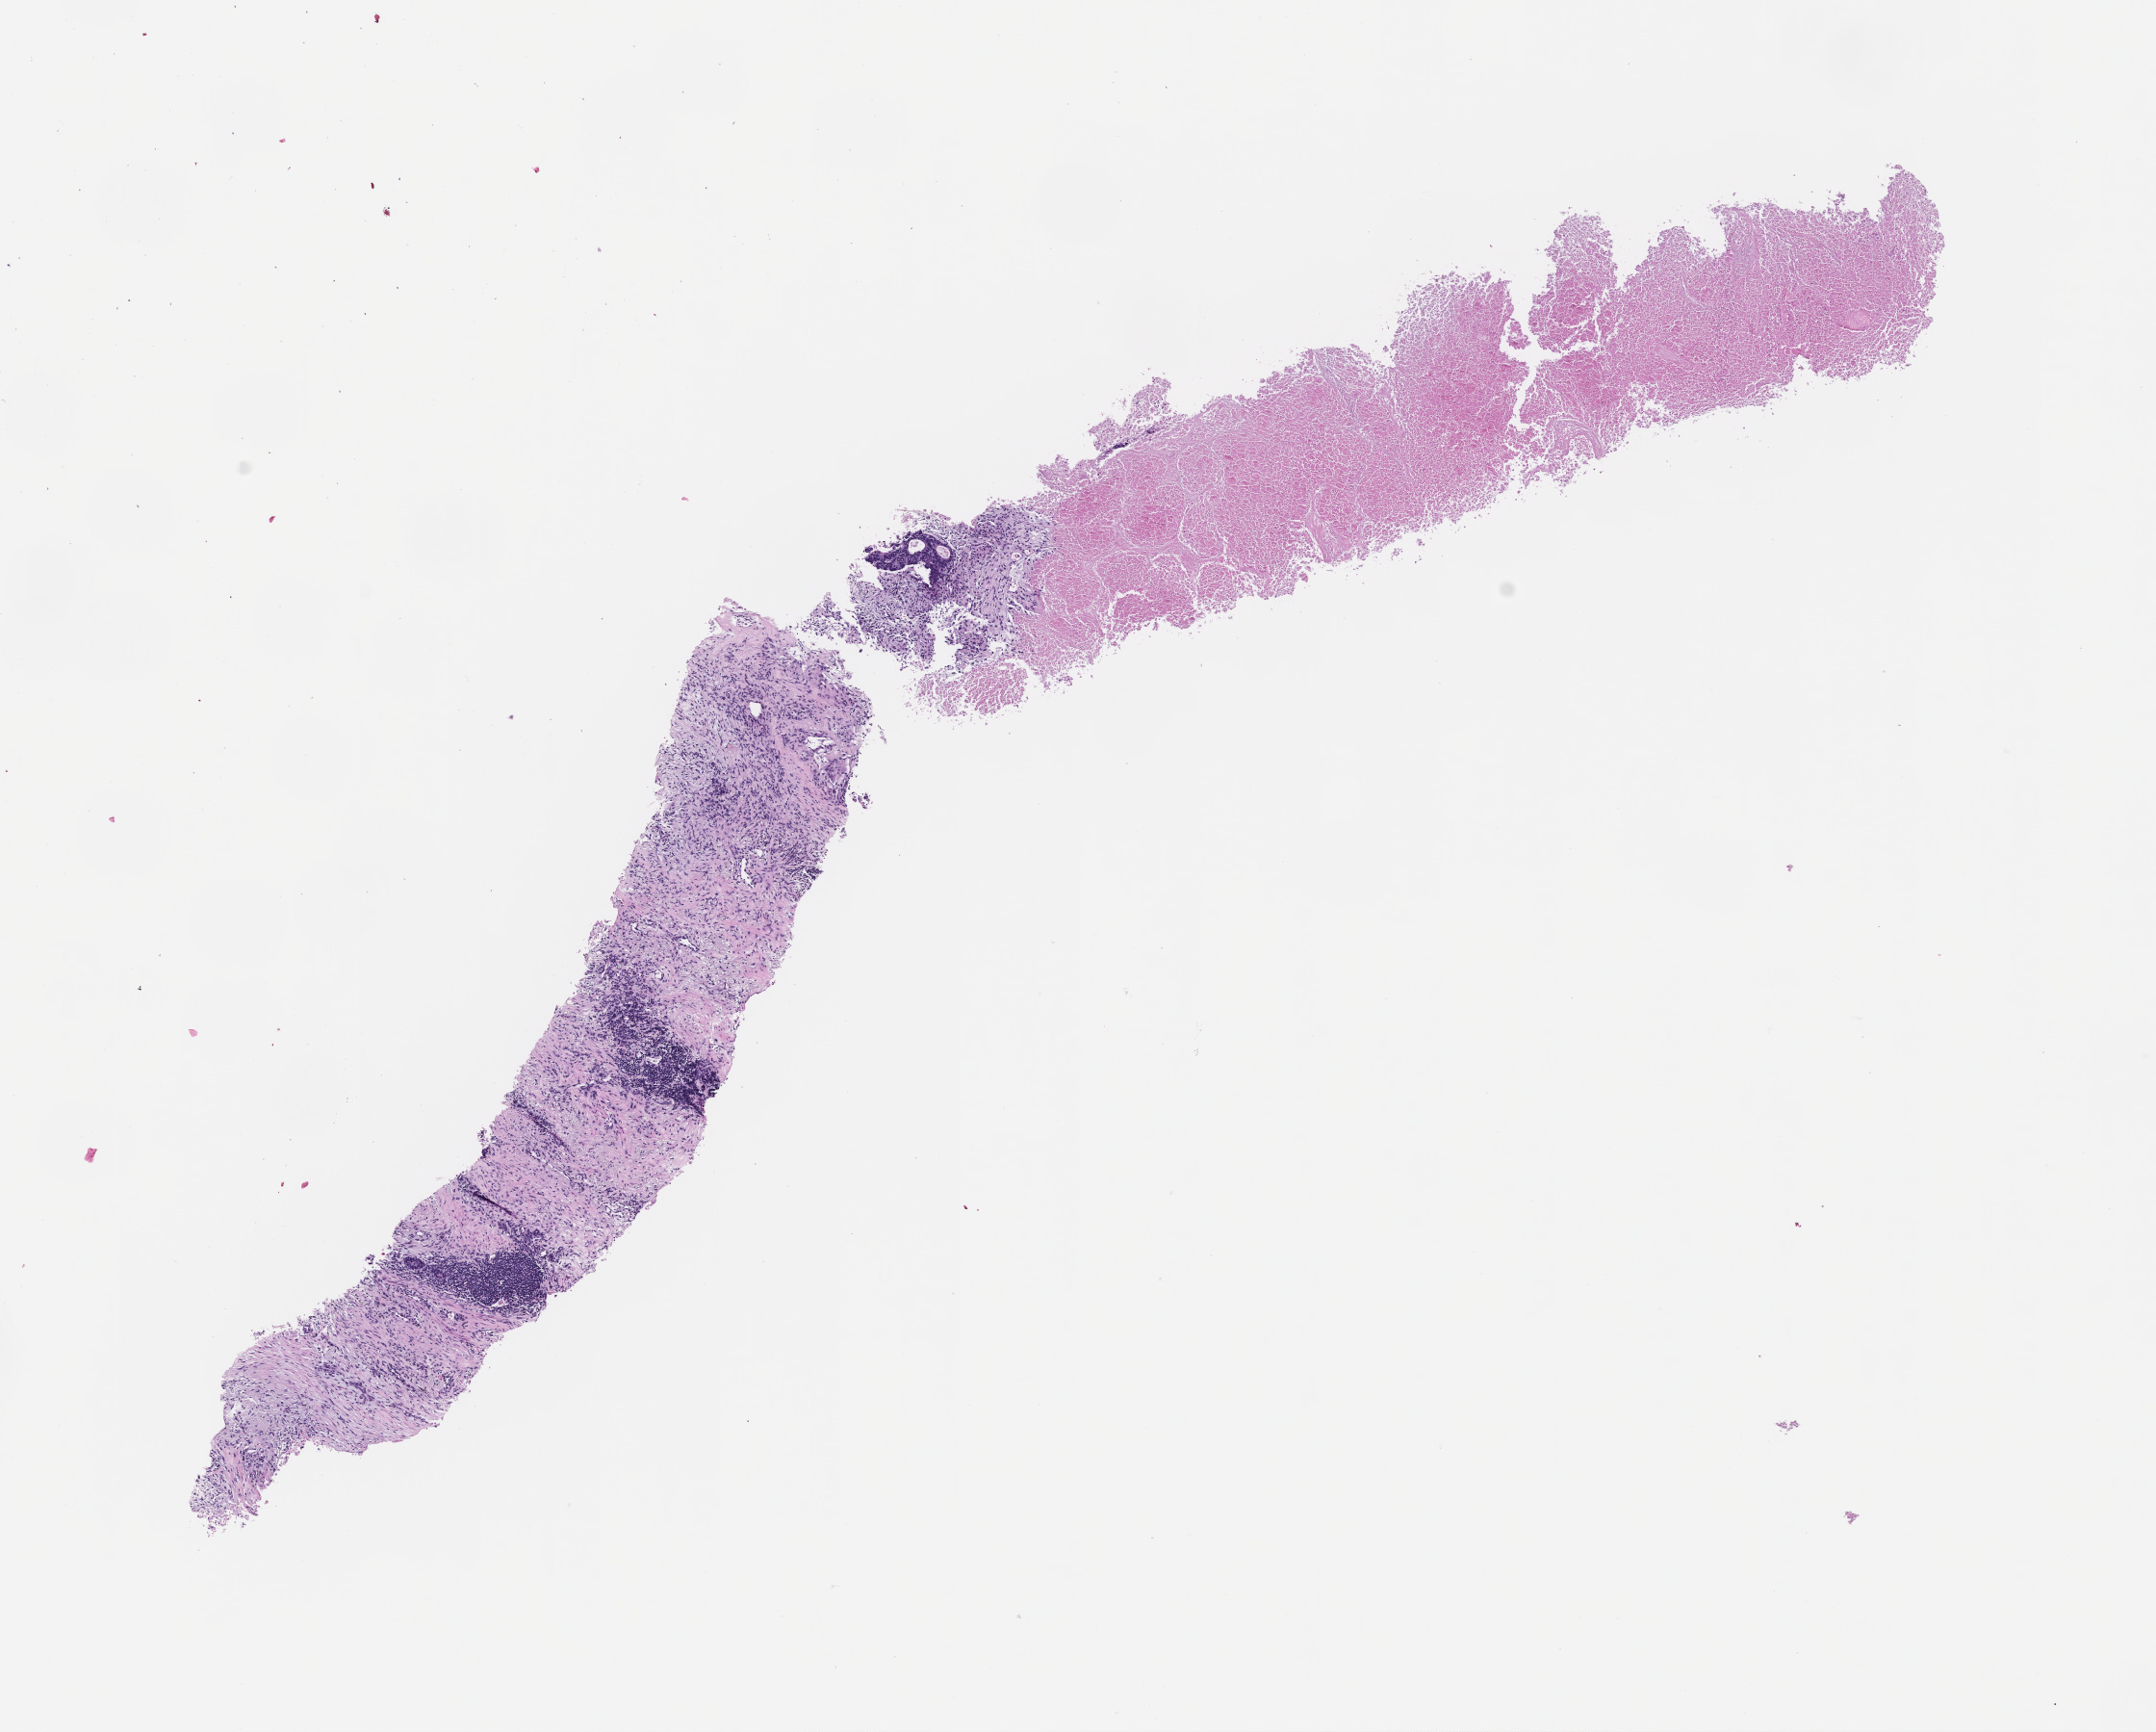
Digitized haematoxylin and eosin-stained section, a low-resolution overview of the entire scanned area, about 9.0 x 7.3 mm, FFPE section. Patient sex: female.
• this section: metastatic tumor tissue
• patient diagnosis (primary): Colorectal Carcinoma